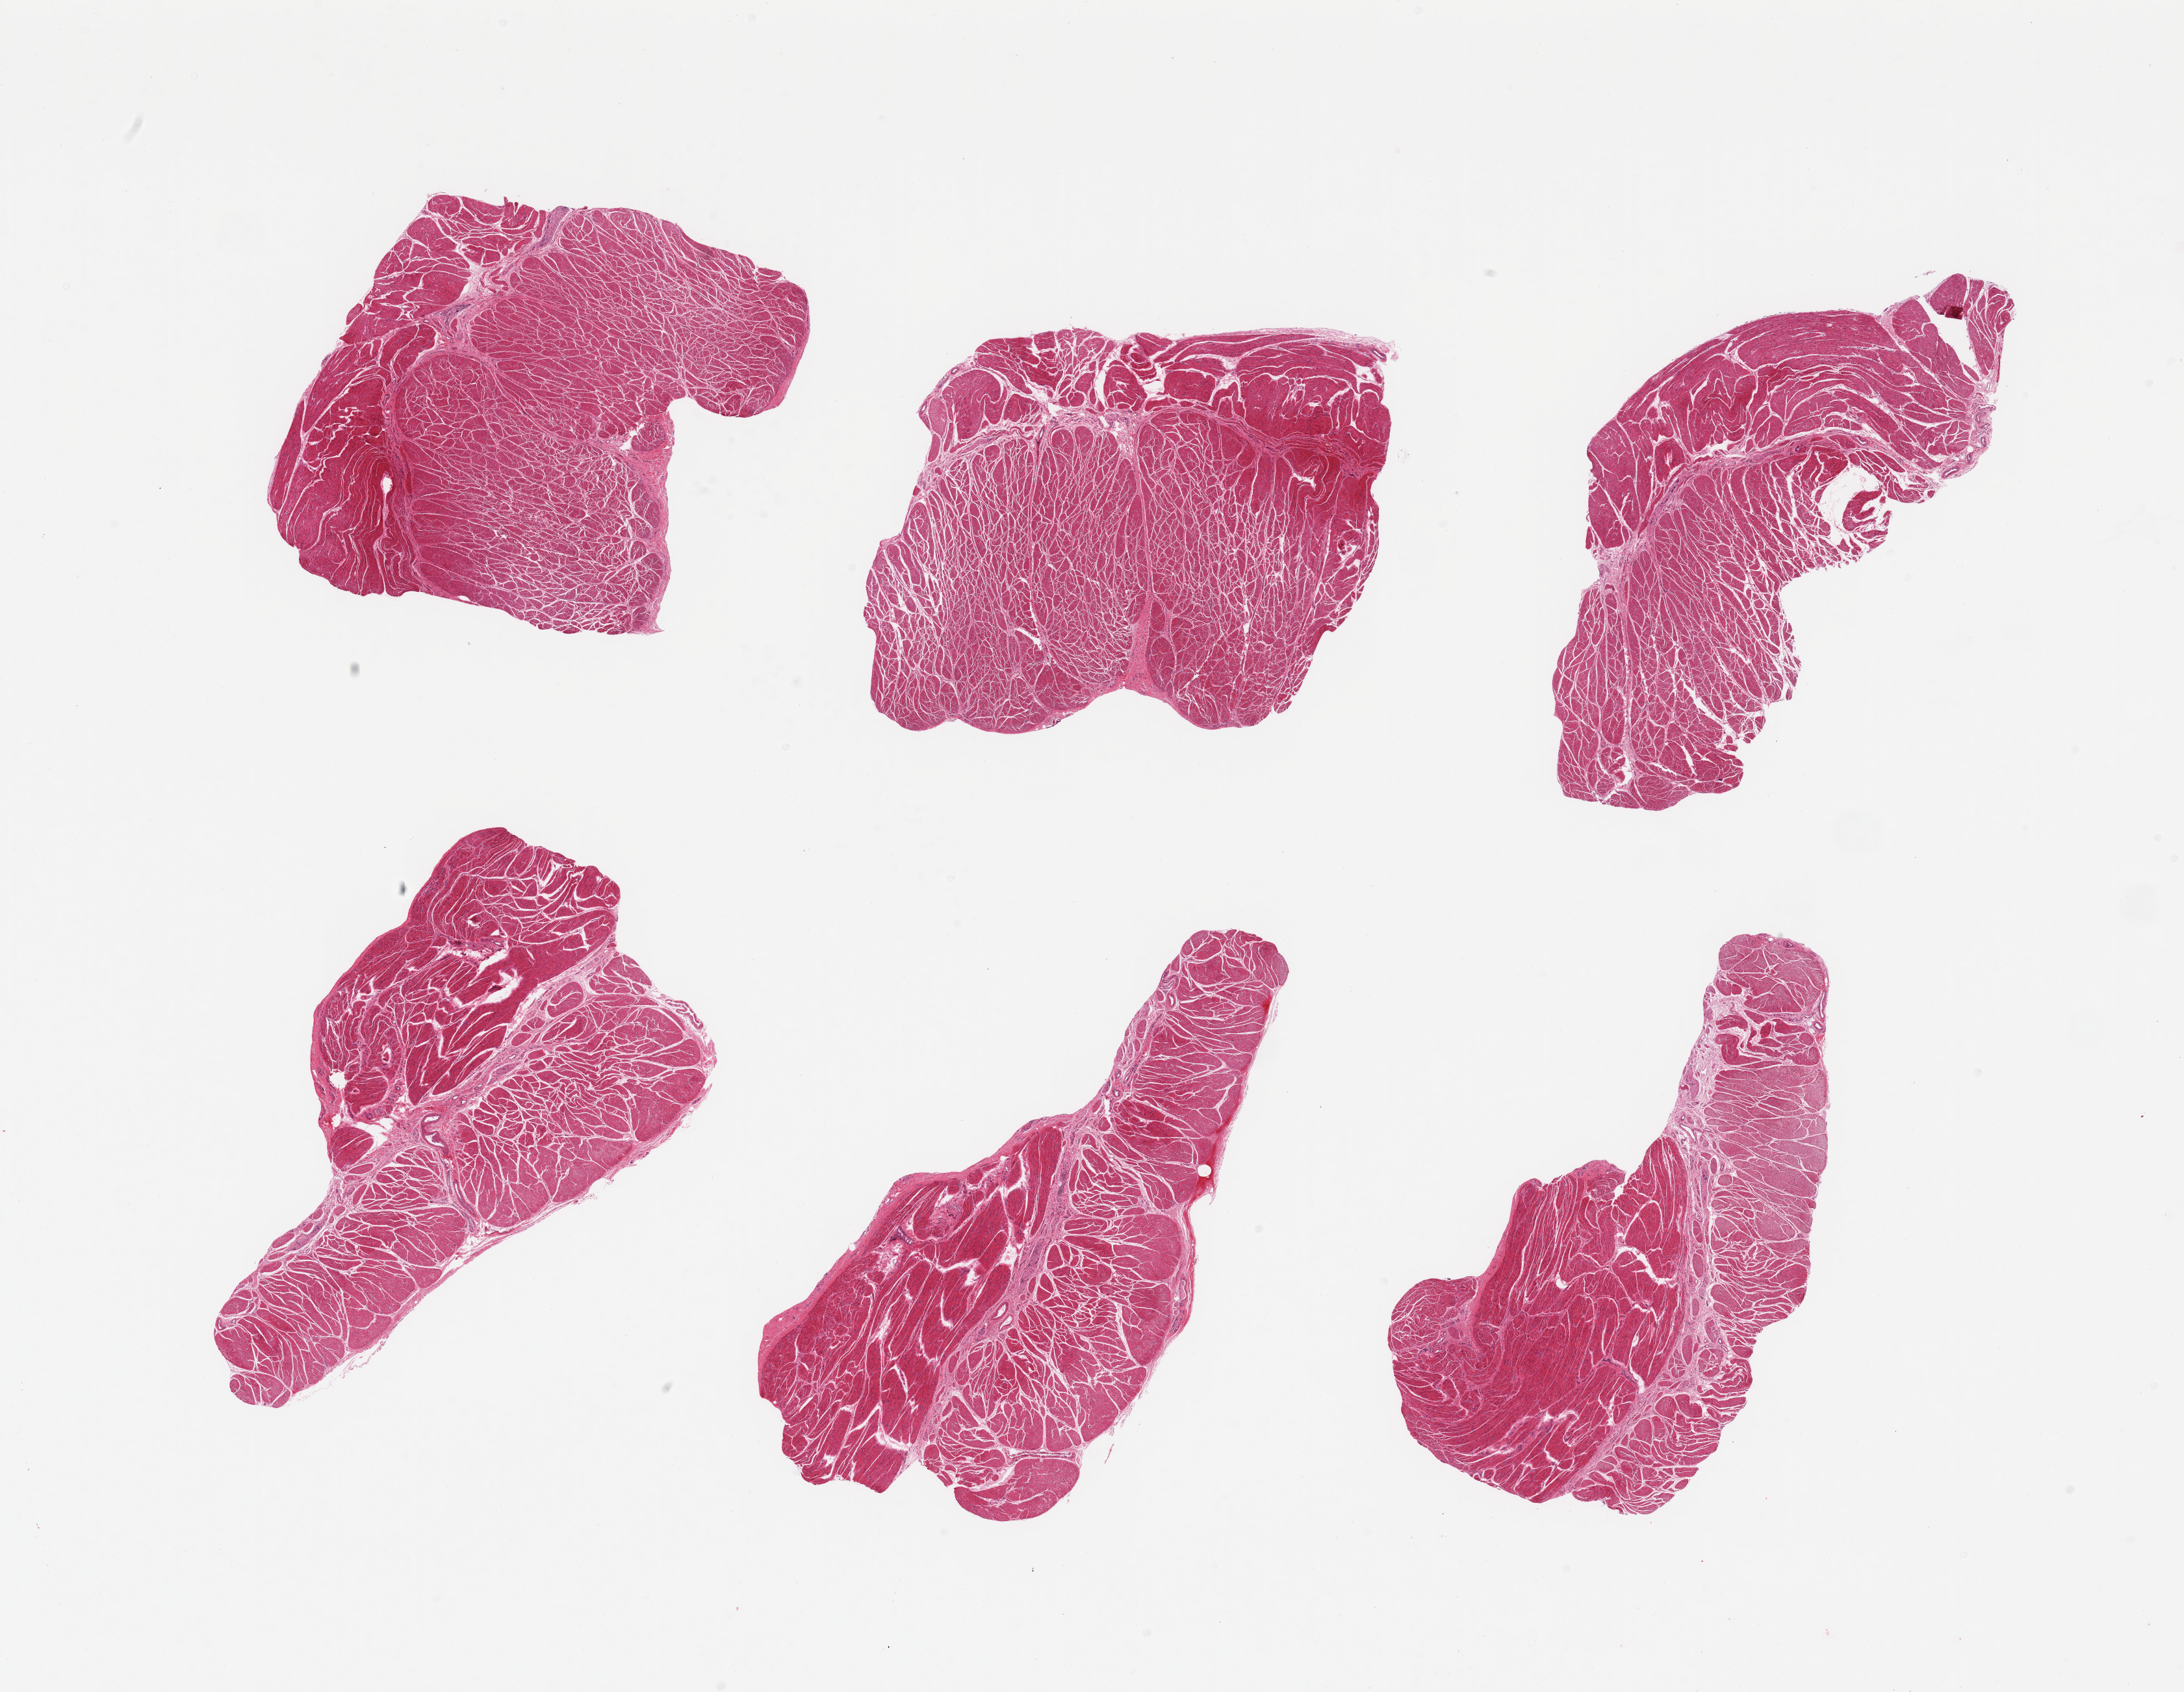
H&E whole-slide image, brightfield, a low-resolution overview of the entire scanned area, about 26.6 x 20.6 mm (slide scanned at 20x); PAXgene-fixed, paraffin-embedded tissue; section of esophageal muscle (target tissue); tissue donor sample. Donor sex: male.
Review note (as recorded): 6 pieces; well trimmed target muscularis.